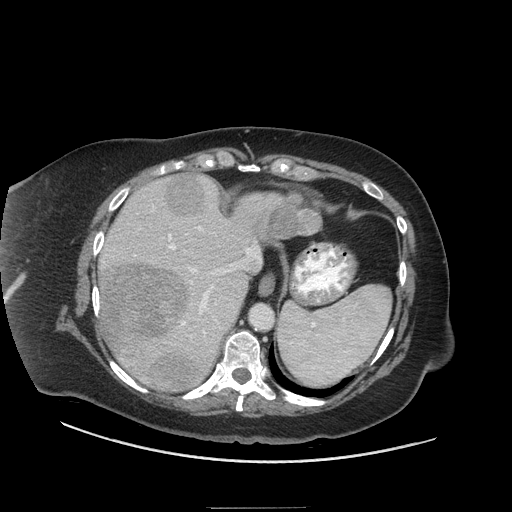
Contrast-enhanced abdominal CT (liver protocol), one axial slice; slice 50 of 81 in the series (ordered by position); 140 kVp; soft-tissue window (W 400 / L 40 HU); 2.5 mm slice thickness; 512 × 512 image matrix, field of view 440 × 440 mm. From the clinical record (not read from this slice): diagnosis: hepatocellular carcinoma (patient treated with transarterial chemoembolisation; whether this scan precedes or follows treatment is not stated here); TNM stage (as recorded): Stage-II; Child-Pugh class: A.
Outlined on this slice (semi-automatically segmented with operator editing):
- liver parenchyma outside the tumour (the mass and vessels are separate outlines, so this box may not span the whole liver): bounding box [x1, y1, x2, y2] px = [99, 174, 282, 392]
- mass: [101, 174, 323, 390]
- liver vessels: [102, 192, 262, 360]